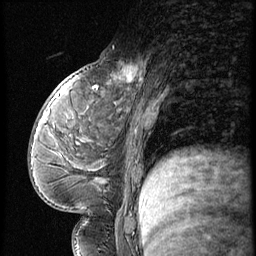
Breast MRI (dynamic contrast-enhanced), one sagittal slice. Position 26 of 56 along the scan axis. 3 images stored at this slice position (order not interpretable as contrast timing). 1.5 T. TE 4.2 ms, TR 9 ms. 256 × 256 image matrix. Patient: female, 54 years. From the clinical record (not read from this slice): setting: breast cancer imaged before/during neoadjuvant chemotherapy; receptor status: triple-negative.
Outlined on this slice (semi-automatic segmentation, software-assisted and operator-edited):
- analysis volume of interest (the breast-tissue region the enhancement analysis was run in; not a lesion): box from (x=99, y=53) to (x=149, y=102) px
- tumour enhancement mask (voxels above the 140 % enhancement threshold inside the analysis volume of interest): (x=113, y=65)–(x=143, y=83)